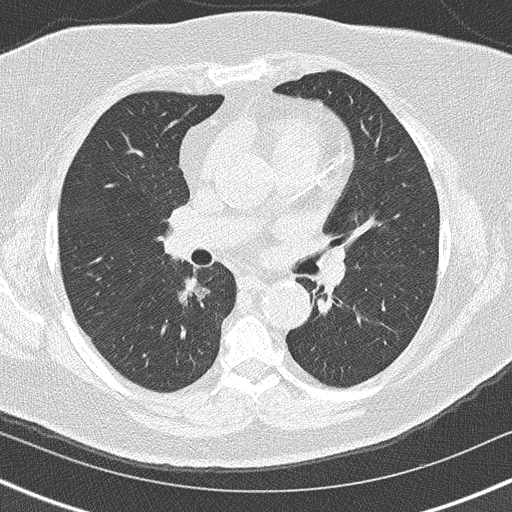
Axial slice from a low-dose chest CT screening exam; second annual screen; lung window (W 1500 / L -600 HU); 2 mm slice thickness; lung (sharp) reconstruction kernel (B50f). Female, age 60 years at enrolment. Former smoker at enrolment.
- Lesion marked by an expert reader, bounding box (x1, y1, x2, y2) in pixels: (150, 264, 212, 321).
- Screening reader's record for this exam (one nodule recorded; not confirmed to be the boxed lesion): non-calcified nodule or mass ≥4 mm, right lower lobe, 20 × 19 mm, soft tissue attenuation, pre-existing on the prior screen: yes; interval growth: yes.
- Participant outcome: lung cancer diagnosed 139 days after this screen — bronchiolo-alveolar carcinoma, non-mucinous, right lower lobe, stage IA (AJCC 6th edition), 15 mm at pathology.